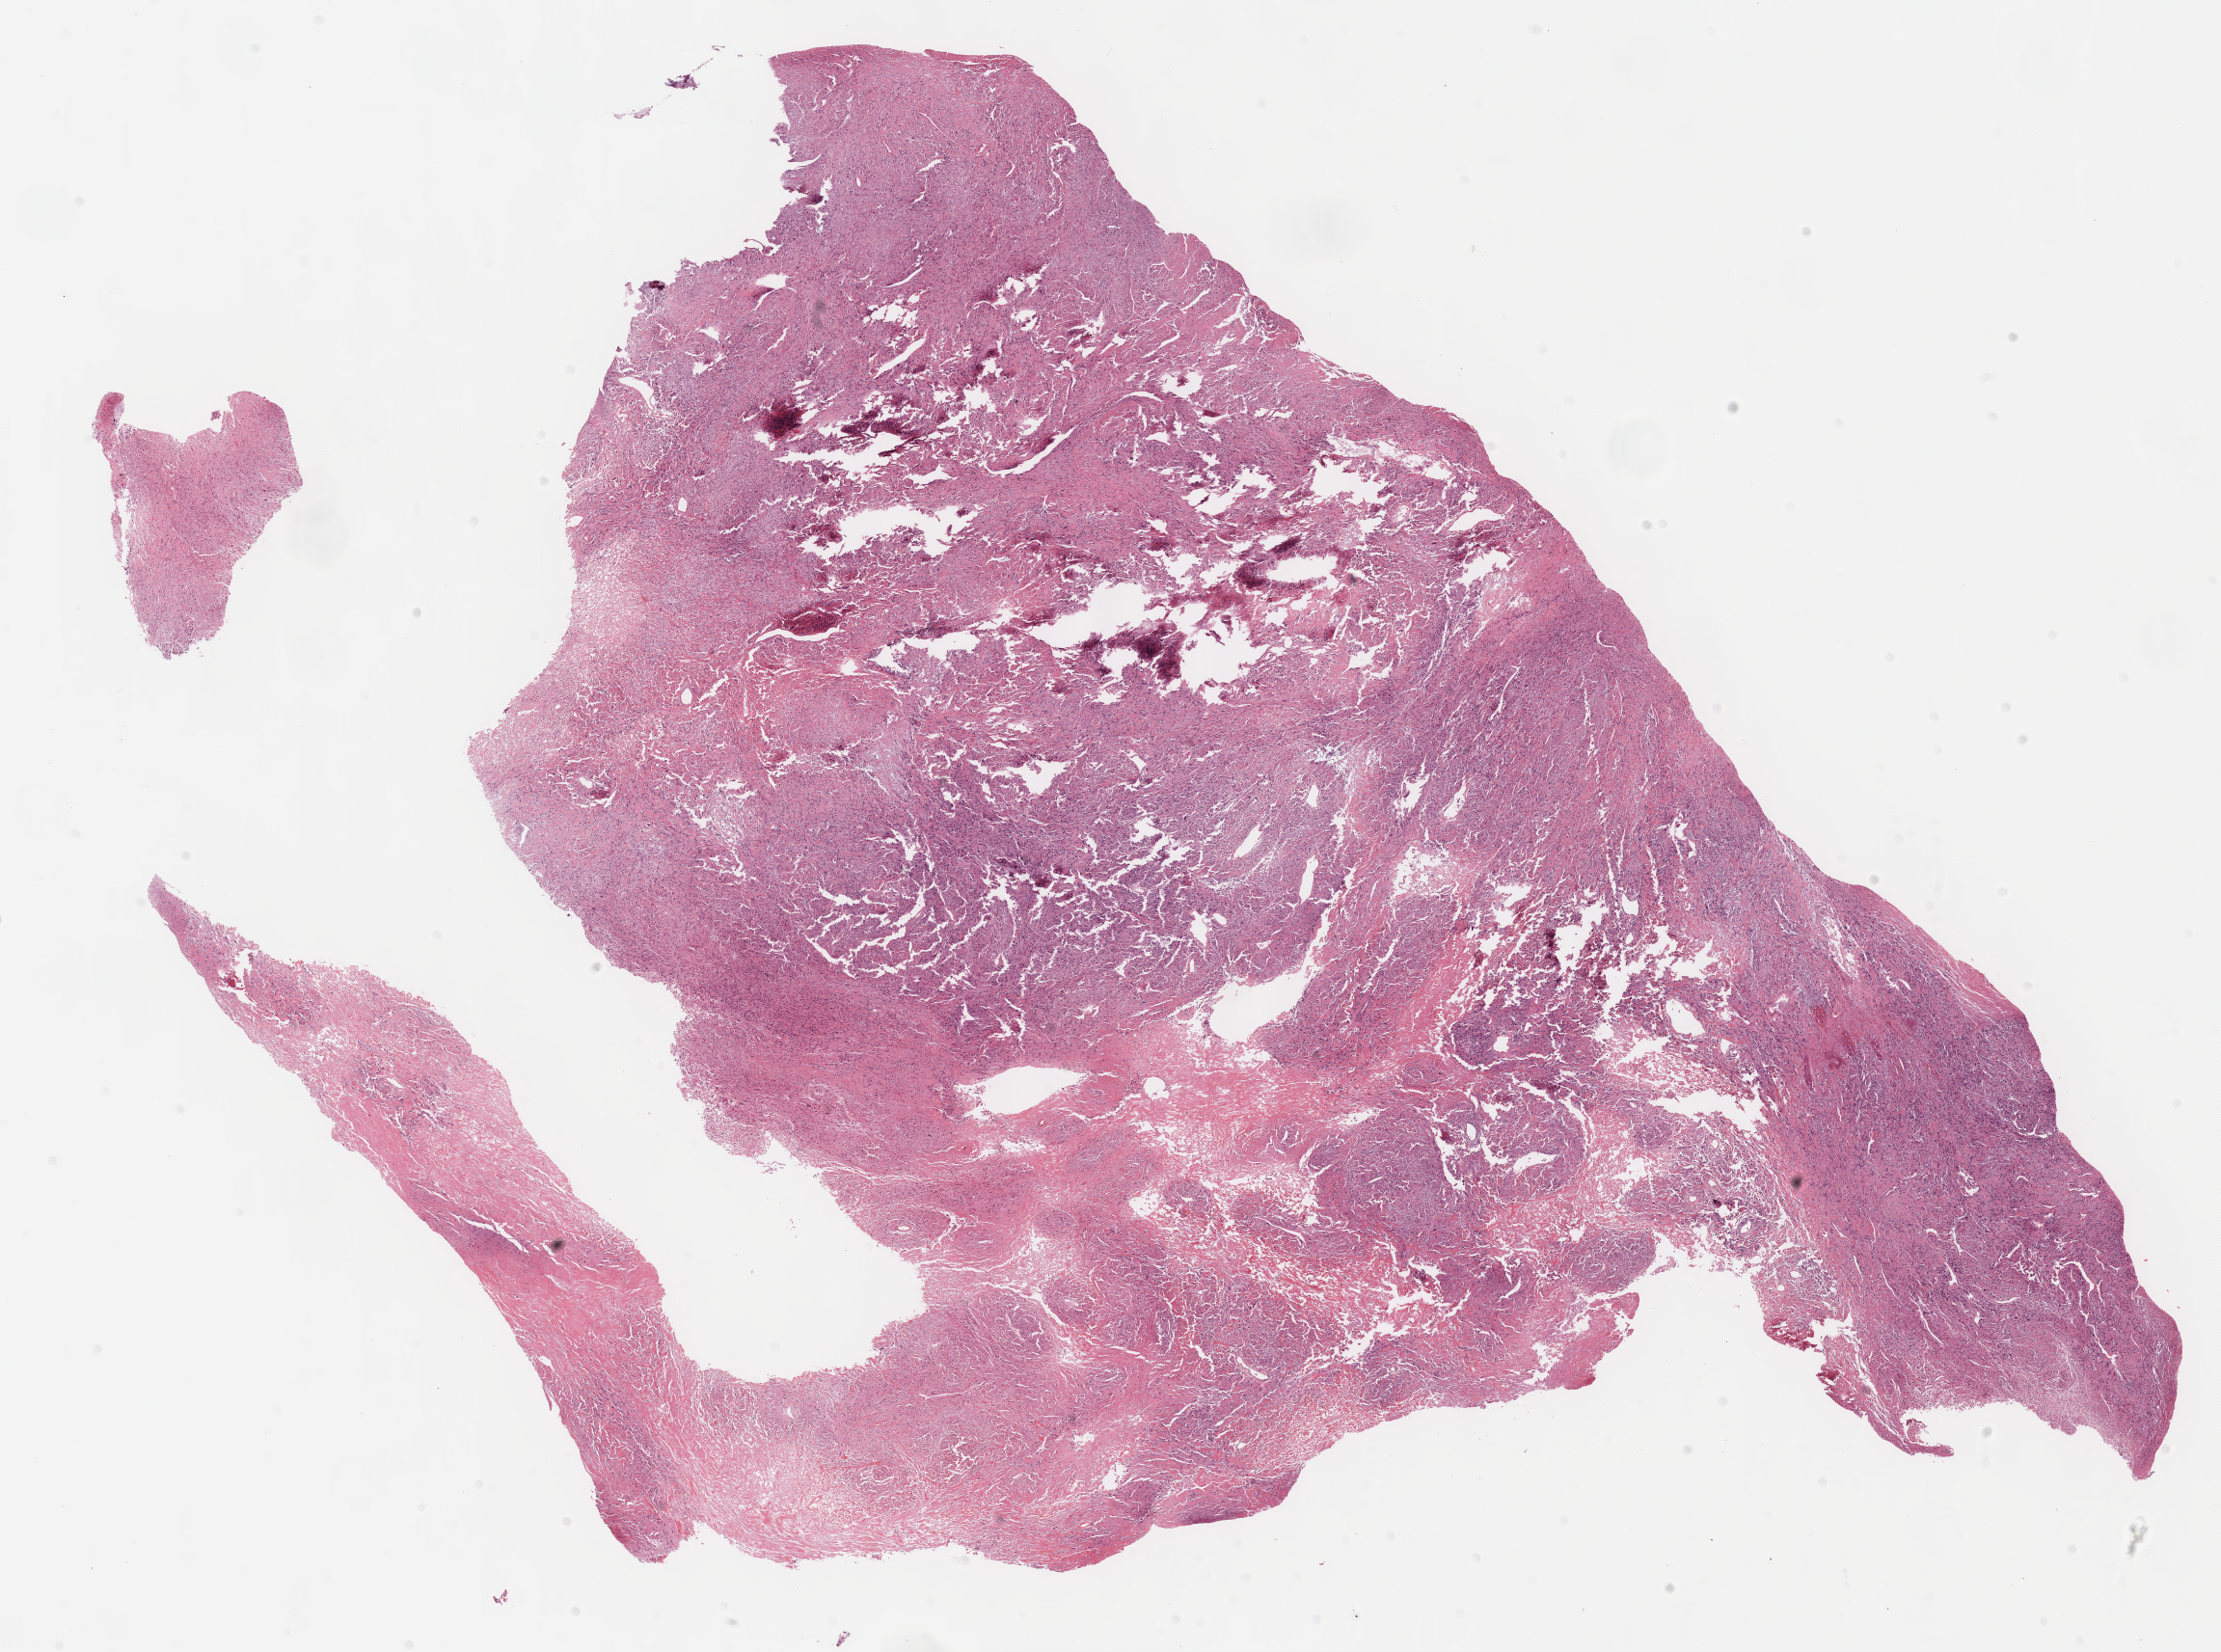
H&E whole-slide image, a low-resolution overview of the entire scanned area, about 18.6 x 13.9 mm (acquisition: 40x scan); formalin-fixed paraffin-embedded (FFPE) diagnostic section; sample: primary tumour, connective, subcutaneous and other soft tissues. Male patient; age at initial diagnosis 58 years.
Pathologic diagnosis: Malignant fibrous histiocytoma (connective, subcutaneous and other soft tissues of lower limb and hip).